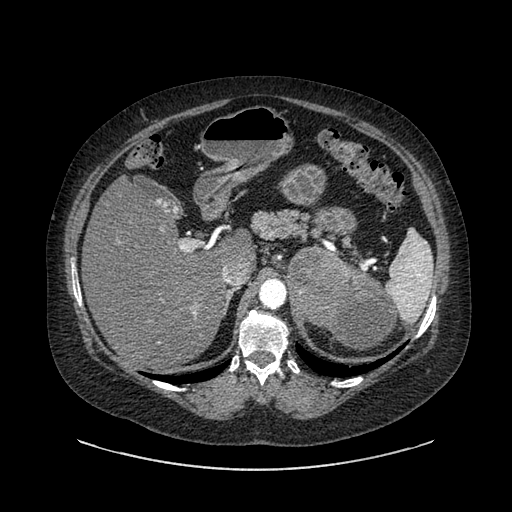
Contrast-enhanced abdominal CT, one axial slice; slice 598 of 769 in the series (ordered by position); reconstruction kernel SOFT; 120 kVp; intravenous contrast given; soft-tissue window (W 400 / L 40 HU); 0.62 mm slice thickness; 512 × 512 image matrix, field of view 460 × 460 mm. Patient: female, 61 years. Case-level facts recorded for this patient, not image findings: diagnosis: adrenocortical carcinoma; tumour side: left adrenal; tumour size at pathology: 13 cm; Ki-67 index: 79 %.
Annotated regions visible in this slice (semi-automatic segmentation, software-assisted and operator-edited):
- mass: bounding box <288,249,394,349> (left, top, right, bottom; pixels)